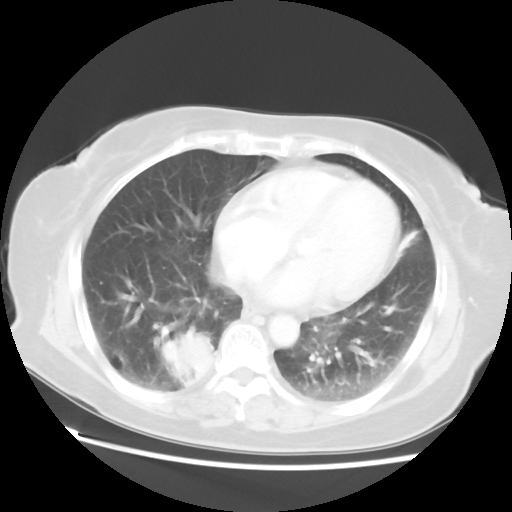
Chest CT, one axial slice; slice 22 of 52 in the series (ordered by position); reconstruction kernel STANDARD; 120 kVp; lung window (W 1500 / L -600 HU); 5 mm slice thickness; 512 × 512 image matrix. Female patient, age 69 years. Case-level facts recorded for this patient, not image findings: clinical TNM (as recorded): T2 N1 M1a.
Annotated regions visible in this slice (rectangle marked by the reading radiologist):
- lung tumour (recorded histology: adenocarcinoma): bounding box [x1, y1, x2, y2] px = [158, 330, 221, 392]